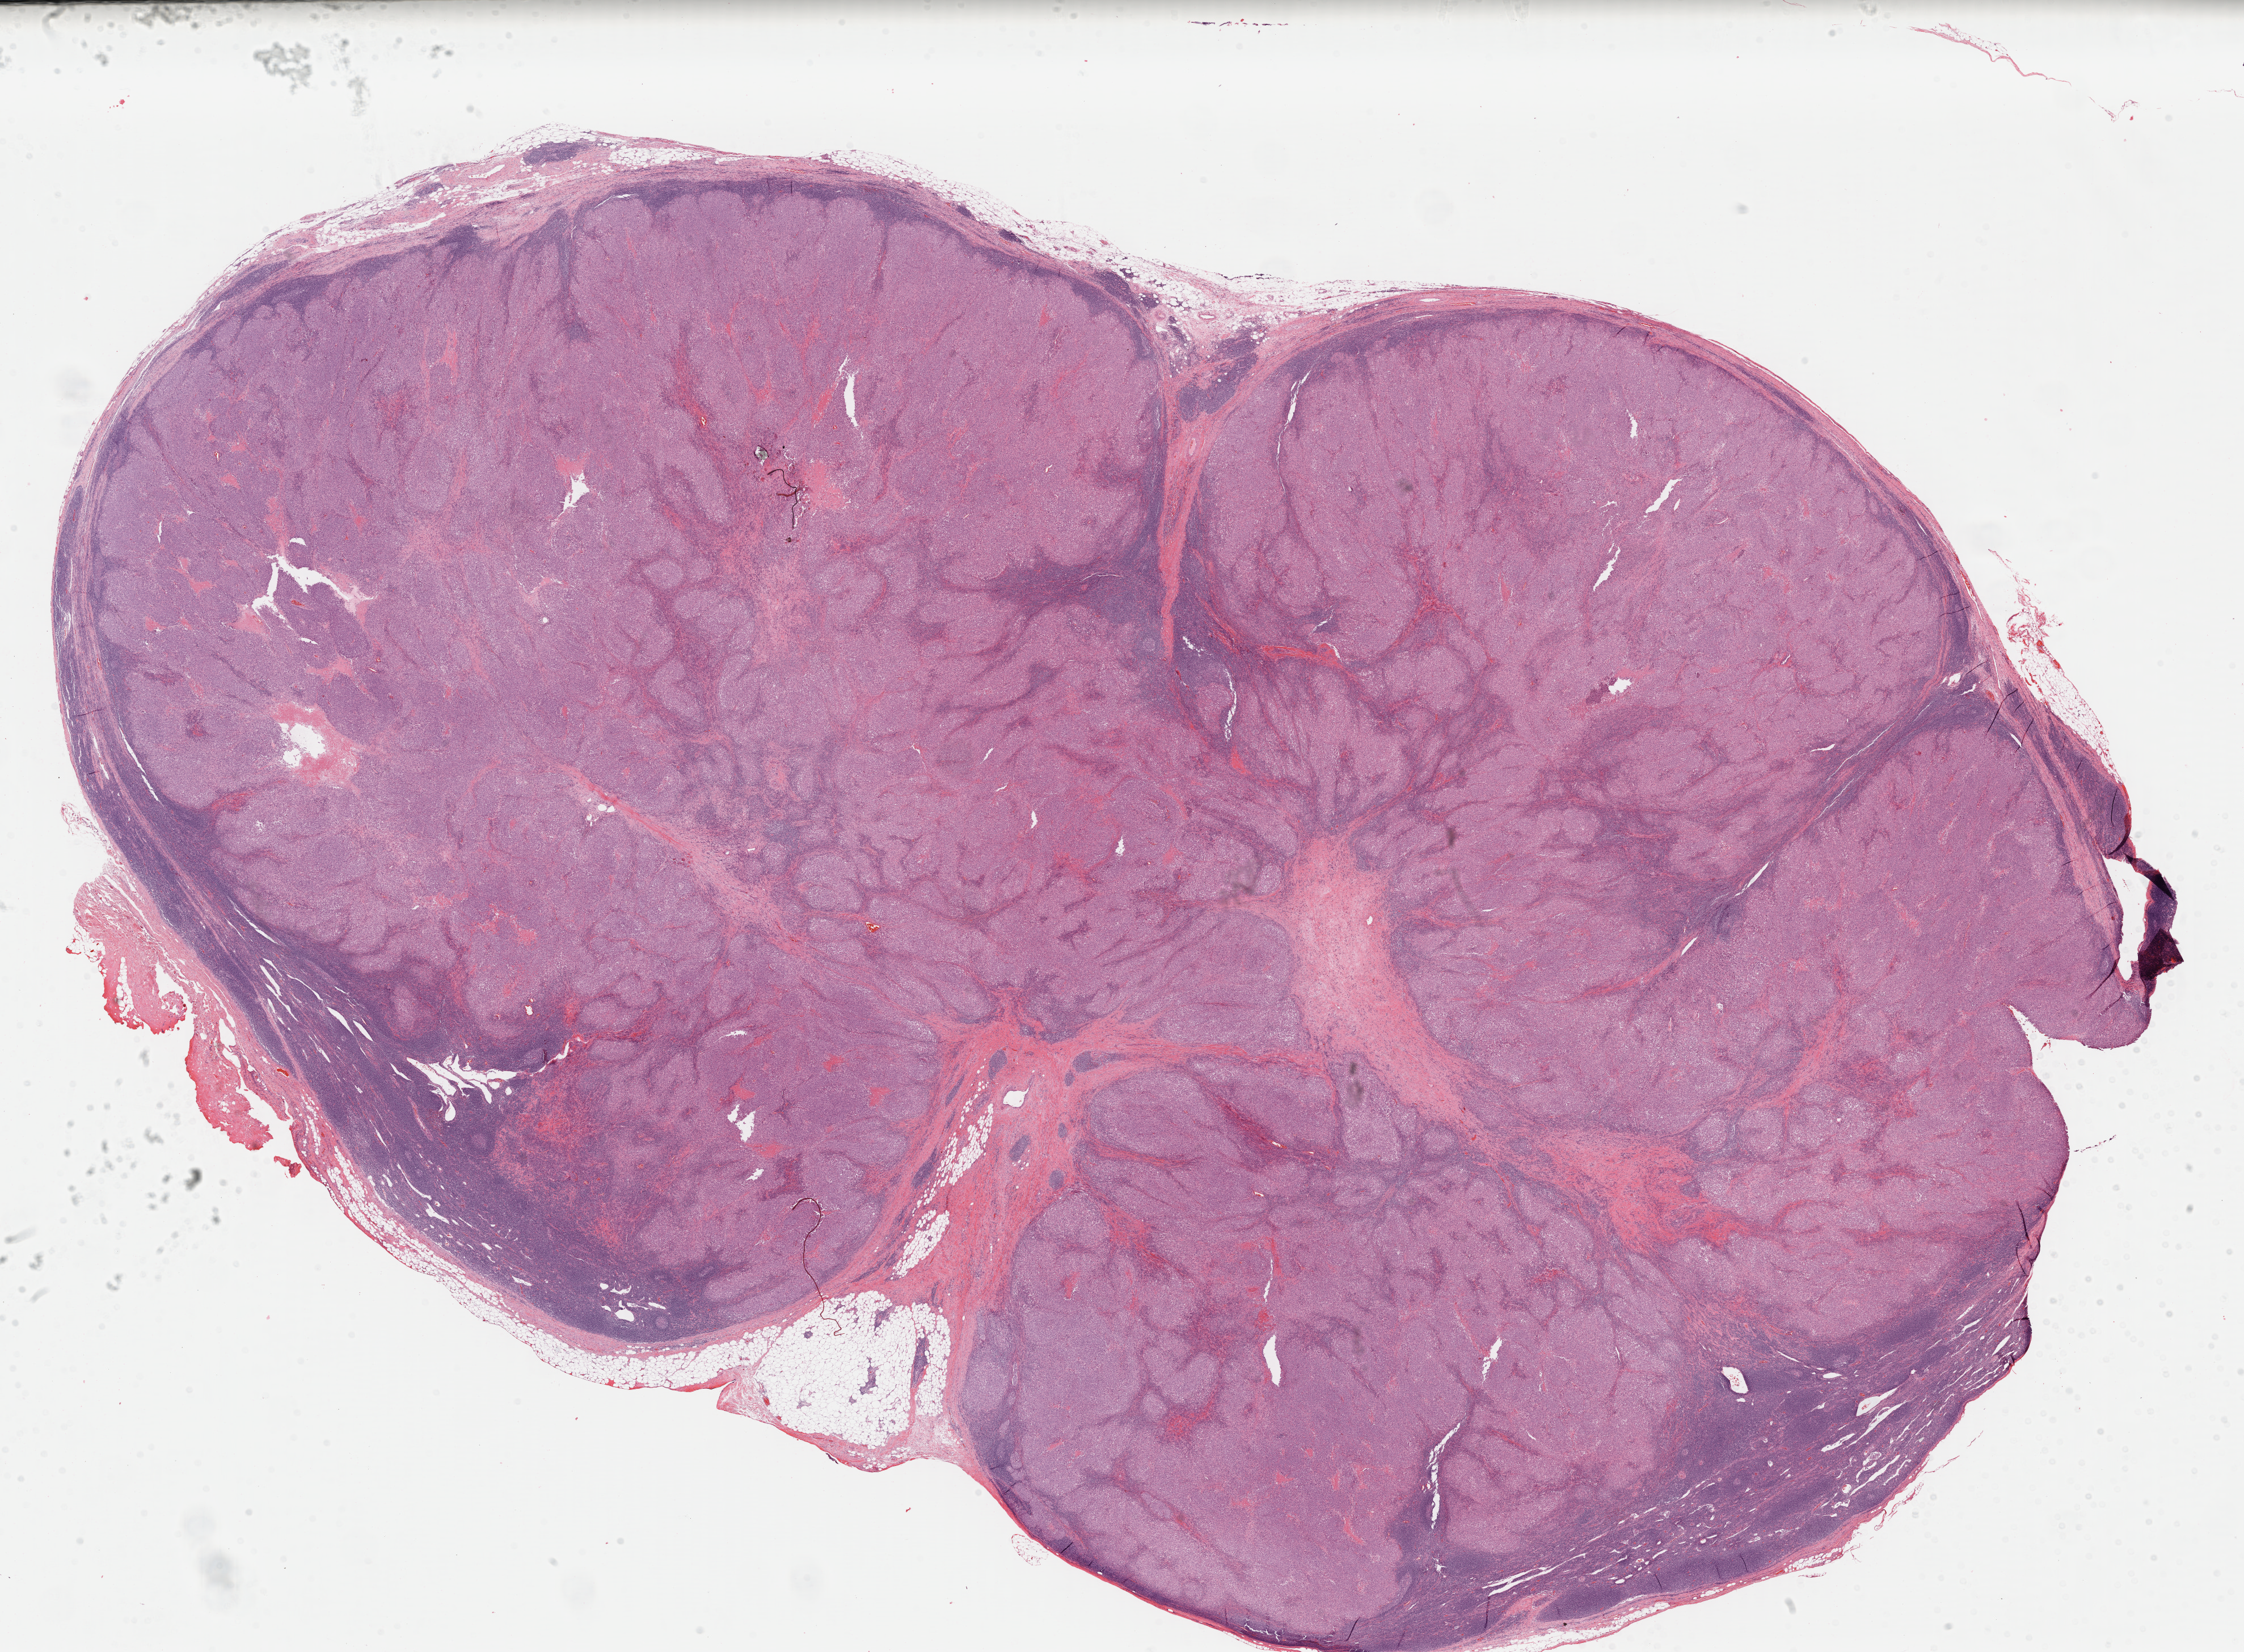
Digitized H&E tissue section (whole slide) — whole scanned area (about 31.2 x 23.0 mm) shown as a low-resolution overview, formalin-fixed paraffin-embedded (FFPE) diagnostic section, metastatic tumour sample, sampled site: lymph nodes of axilla or arm. Male patient; age at initial diagnosis 51 years.
* this section: metastatic tumour tissue
* patient diagnosis: Malignant melanoma, NOS